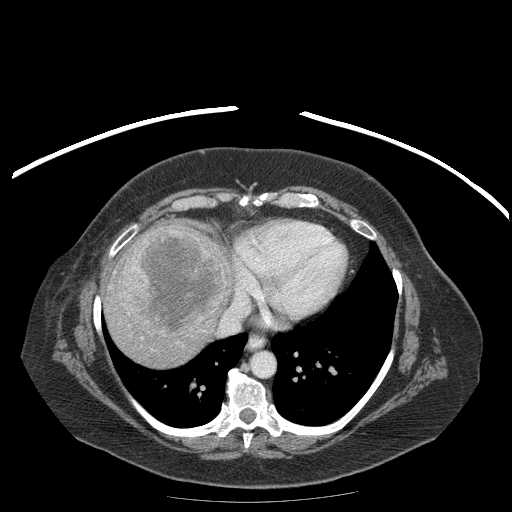
Contrast-enhanced abdominal CT (liver protocol), one axial slice; position 163 of 204 along the scan axis; 120 kVp; soft-tissue window (W 400 / L 40 HU); 512 × 512 image matrix, field of view 440 × 440 mm. From the clinical record (not read from this slice): diagnosis: hepatocellular carcinoma (patient treated with transarterial chemoembolisation; whether this scan precedes or follows treatment is not stated here); TNM stage (as recorded): Stage-IIIB.
Structures marked on this image (semi-automatically segmented with operator editing):
- liver parenchyma outside the tumour (the mass and vessels are separate outlines, so this box may not span the whole liver): bounding box (x1, y1, x2, y2) in pixels: (102, 222, 232, 368)
- mass: (120, 228, 227, 337)